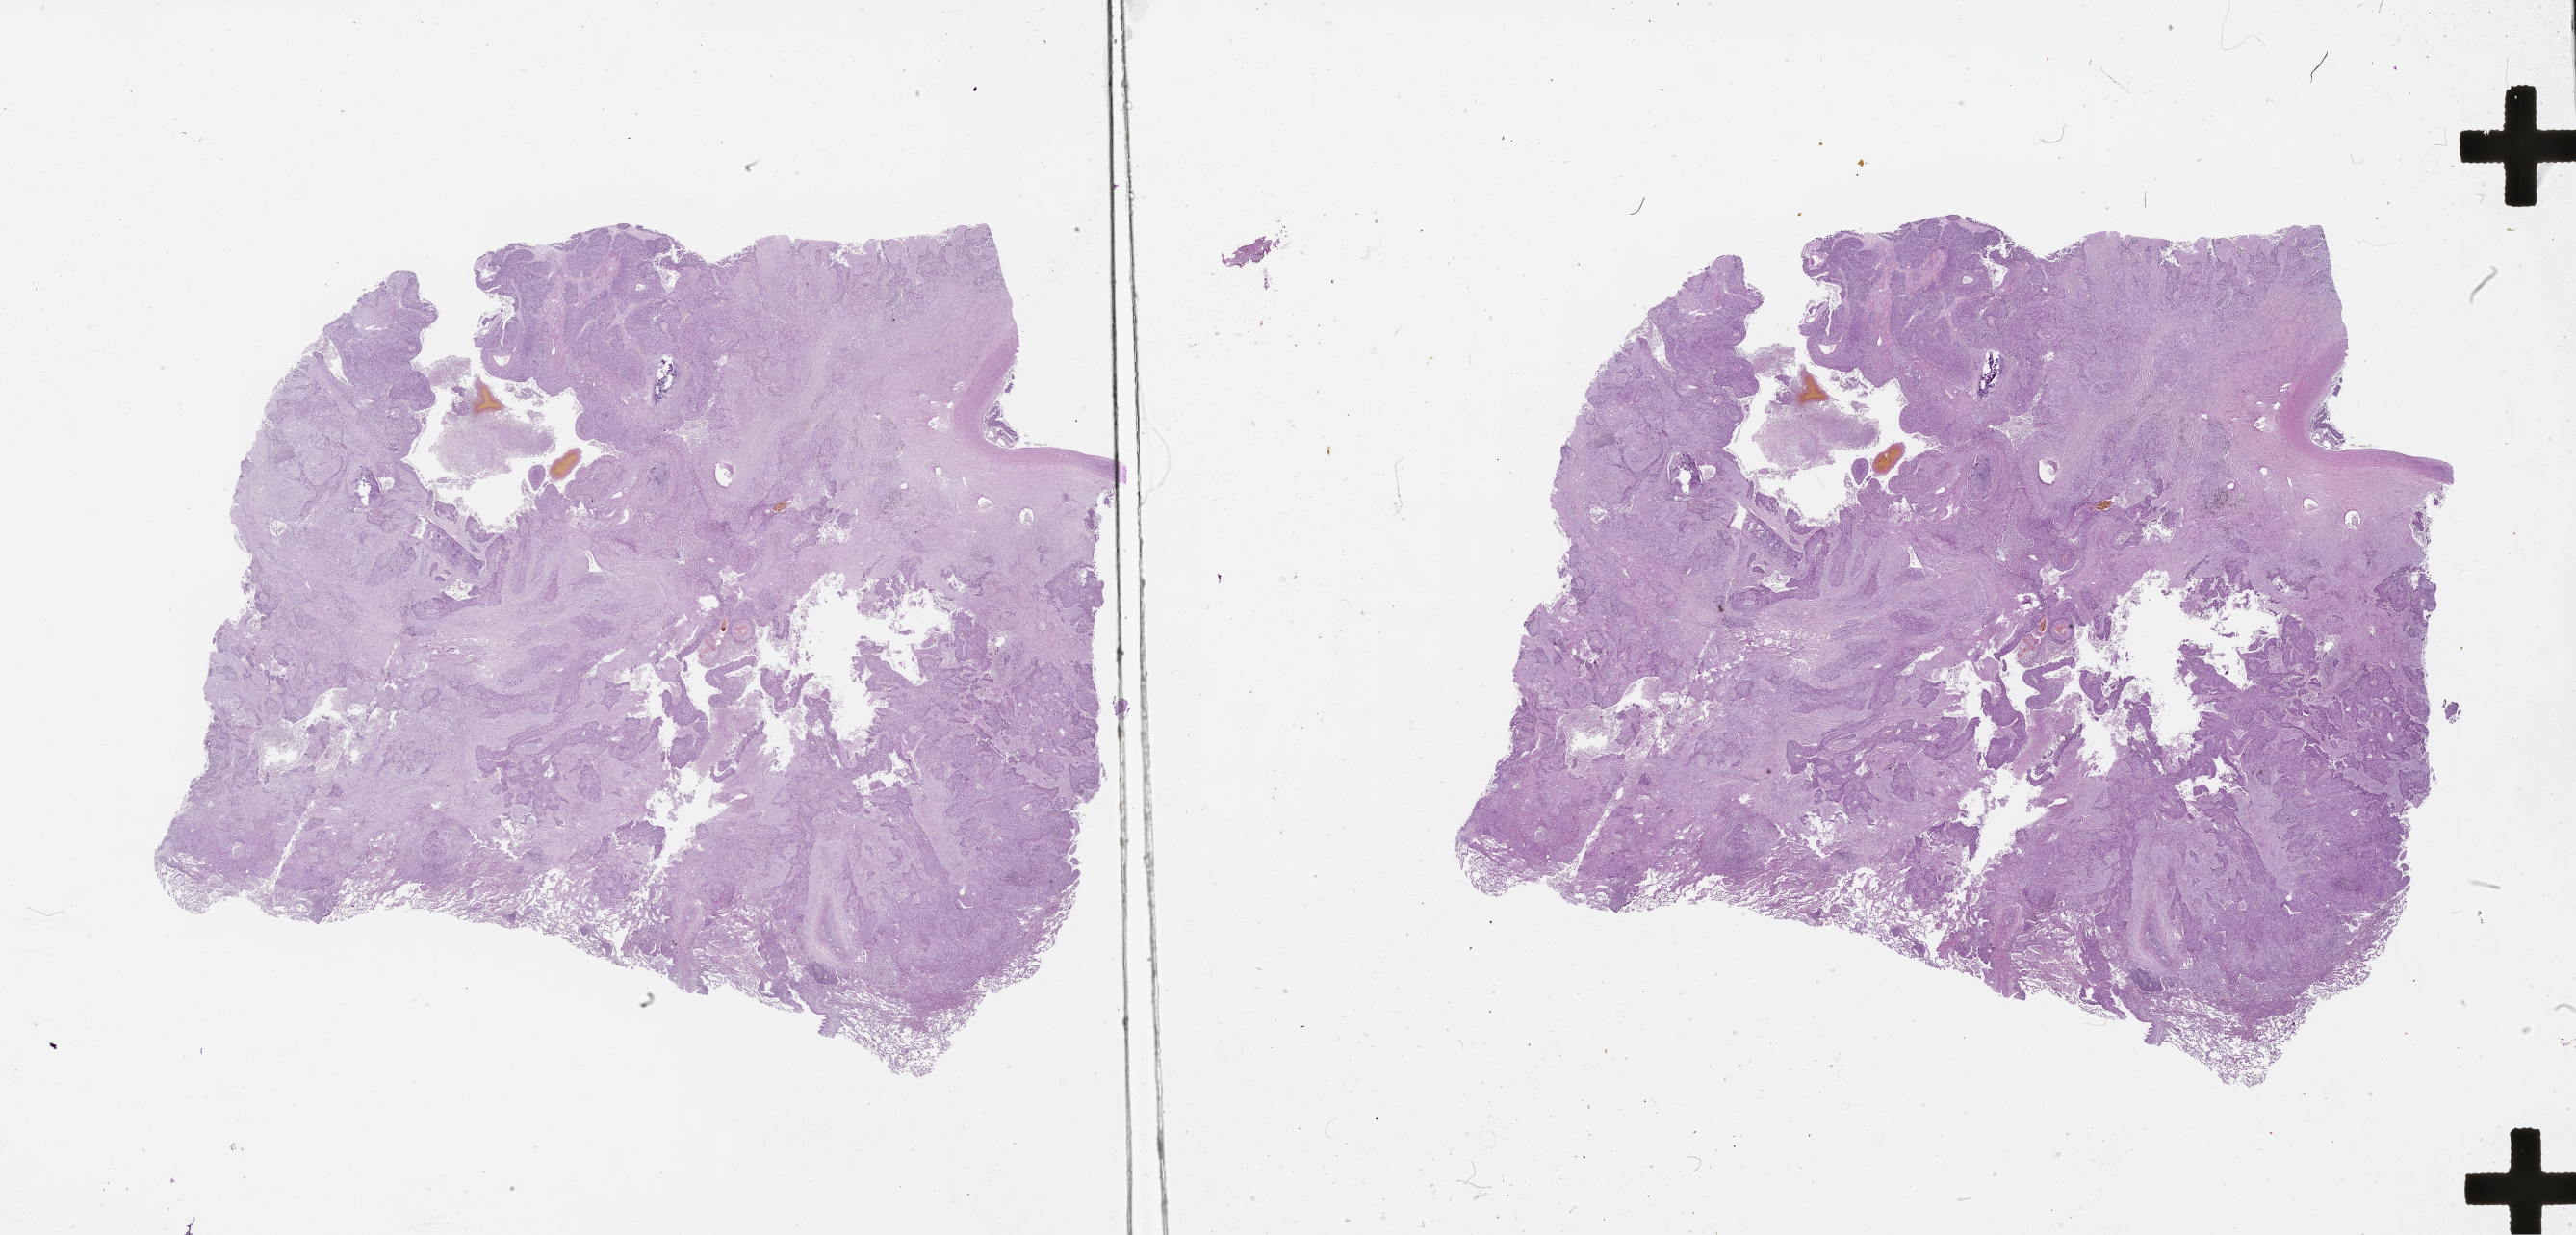
Digitized Hematoxylin and eosin (H&E) stained tissue section (whole slide), low-resolution overview of the scanned area, about 43.1 x 20.7 mm; lung, tumour tissue. Male, 65 y/o.
Patient diagnosis (cohort enrolment): squamous cell carcinoma (lung).